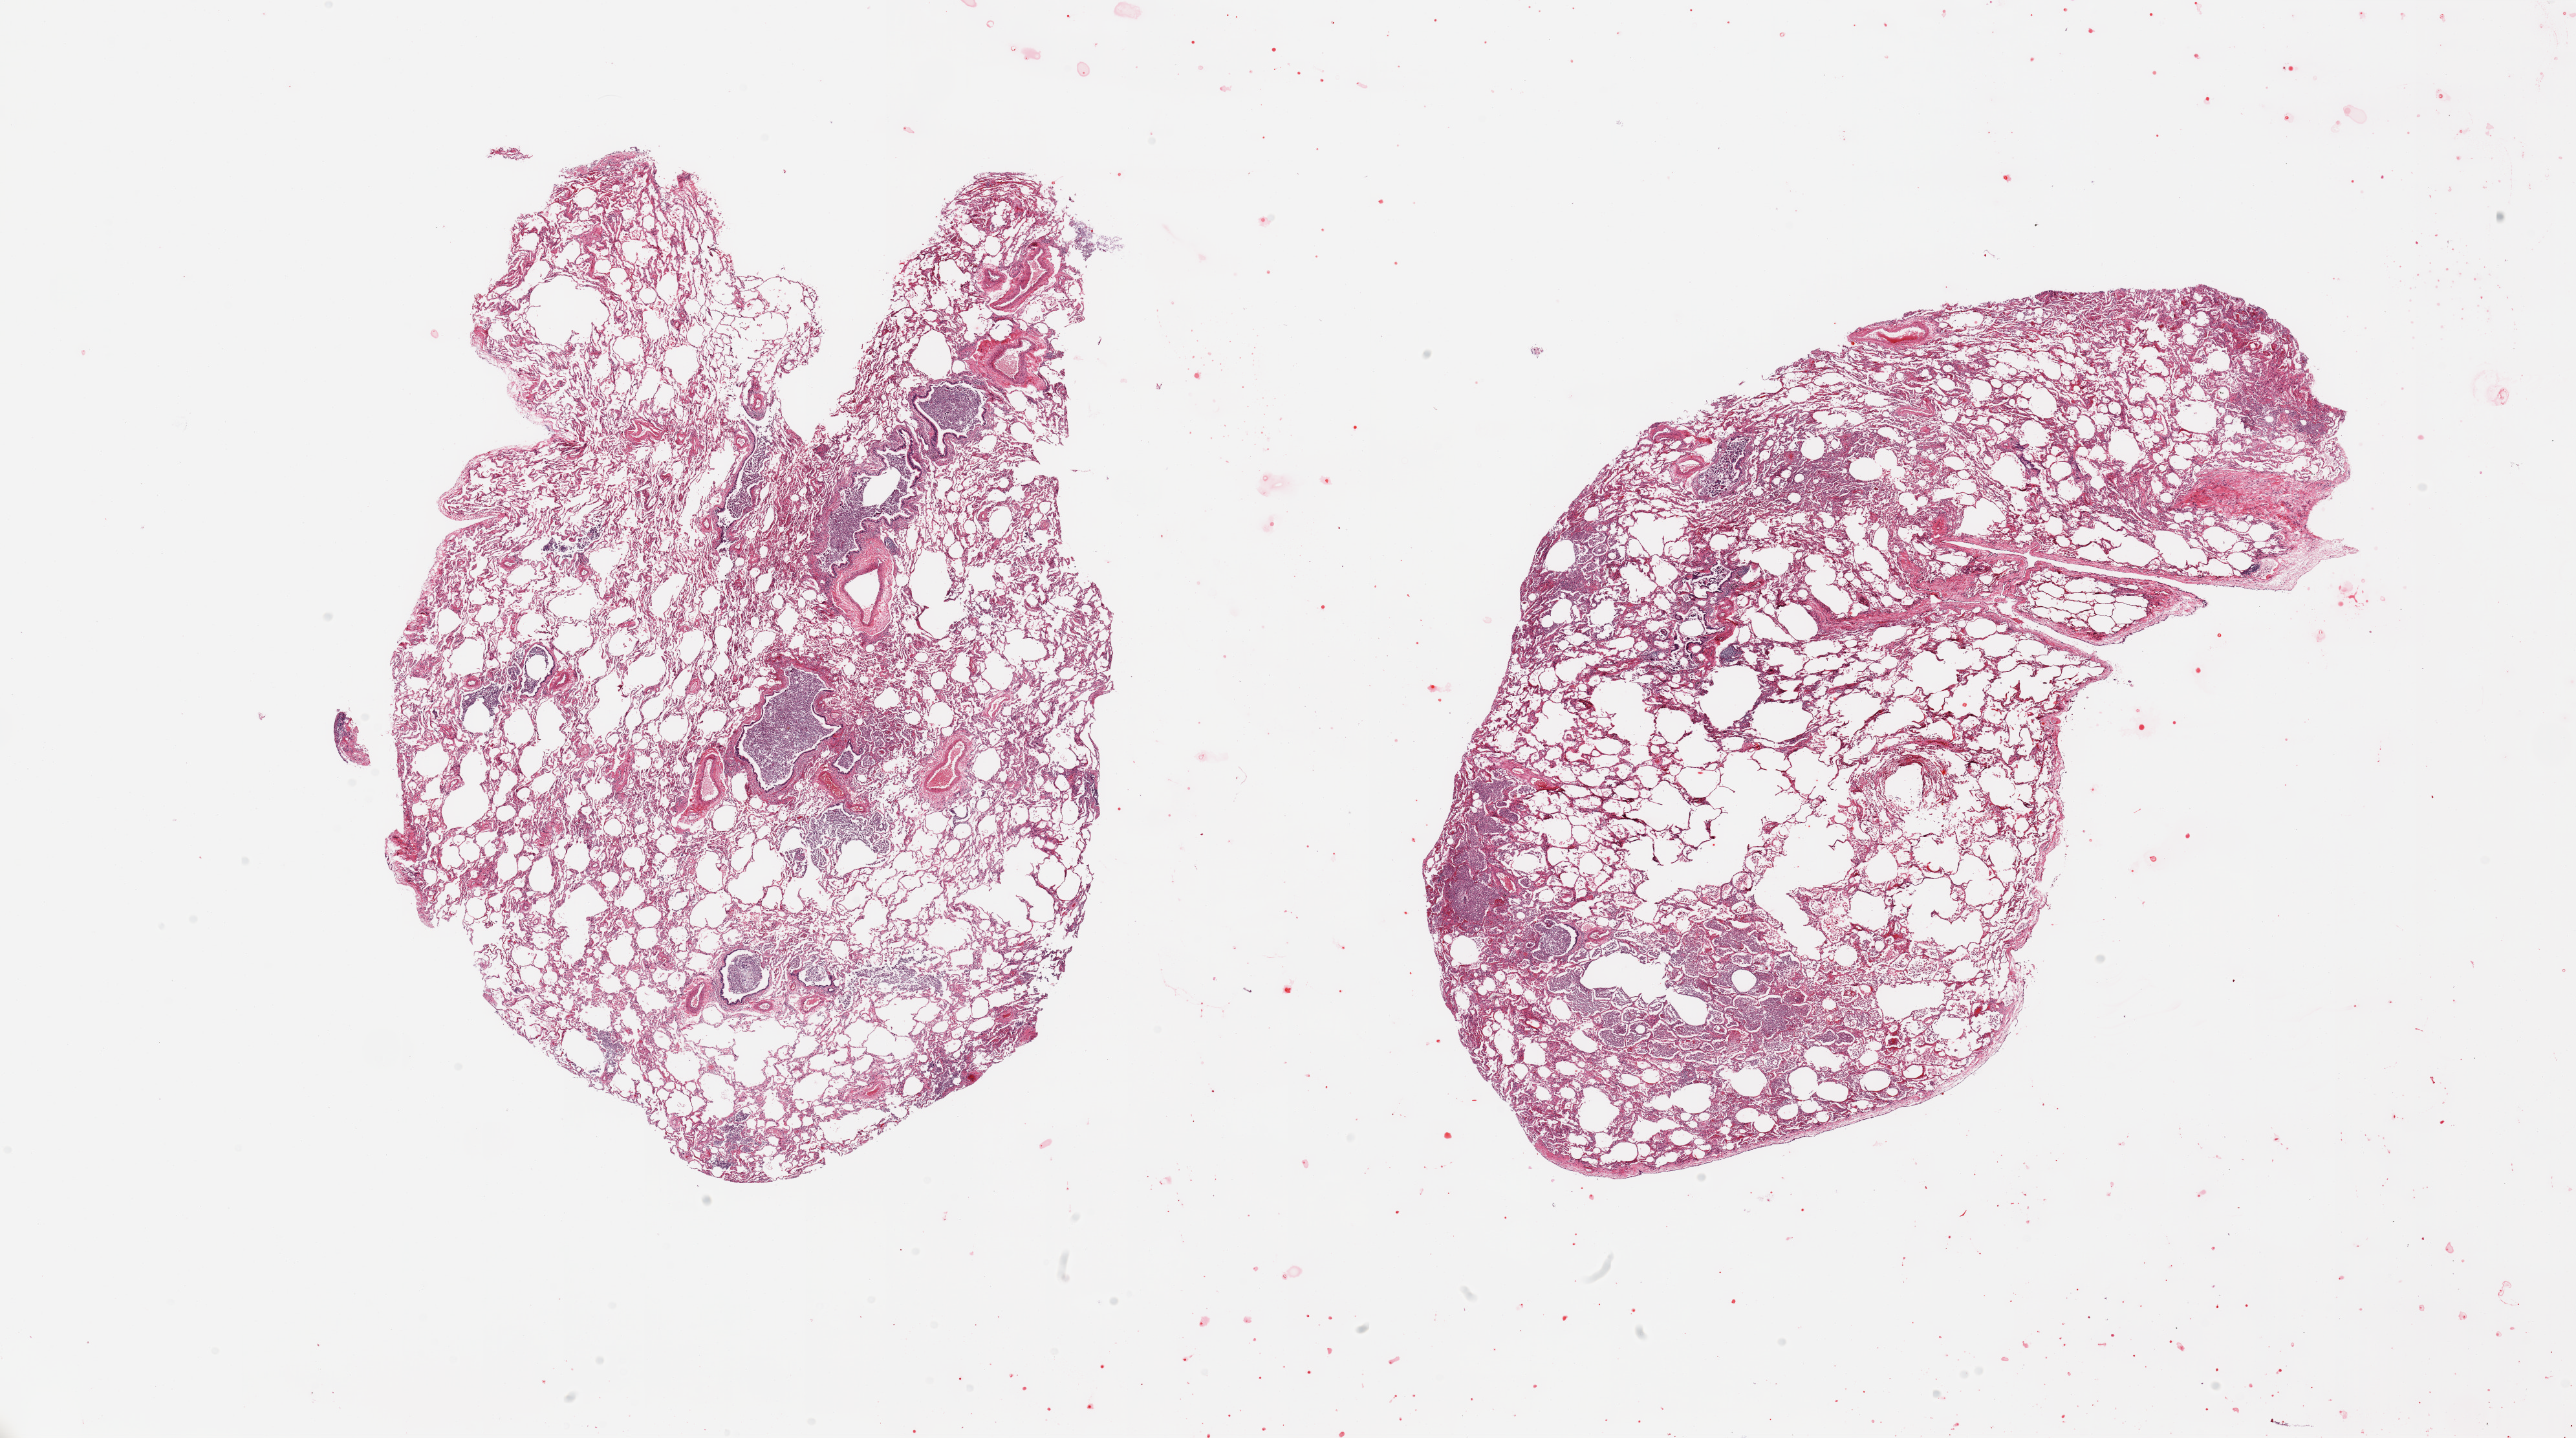
Haematoxylin and eosin whole-slide image — shown as a low-resolution overview of the whole scanned area (about 31.5 x 17.6 mm); PAXgene-fixed paraffin-embedded (PFPE) section; sampled site (target tissue): lung; donor tissue sample. Male donor.
Review note (as recorded): 2 pieces; extensive bronchopneumonia.